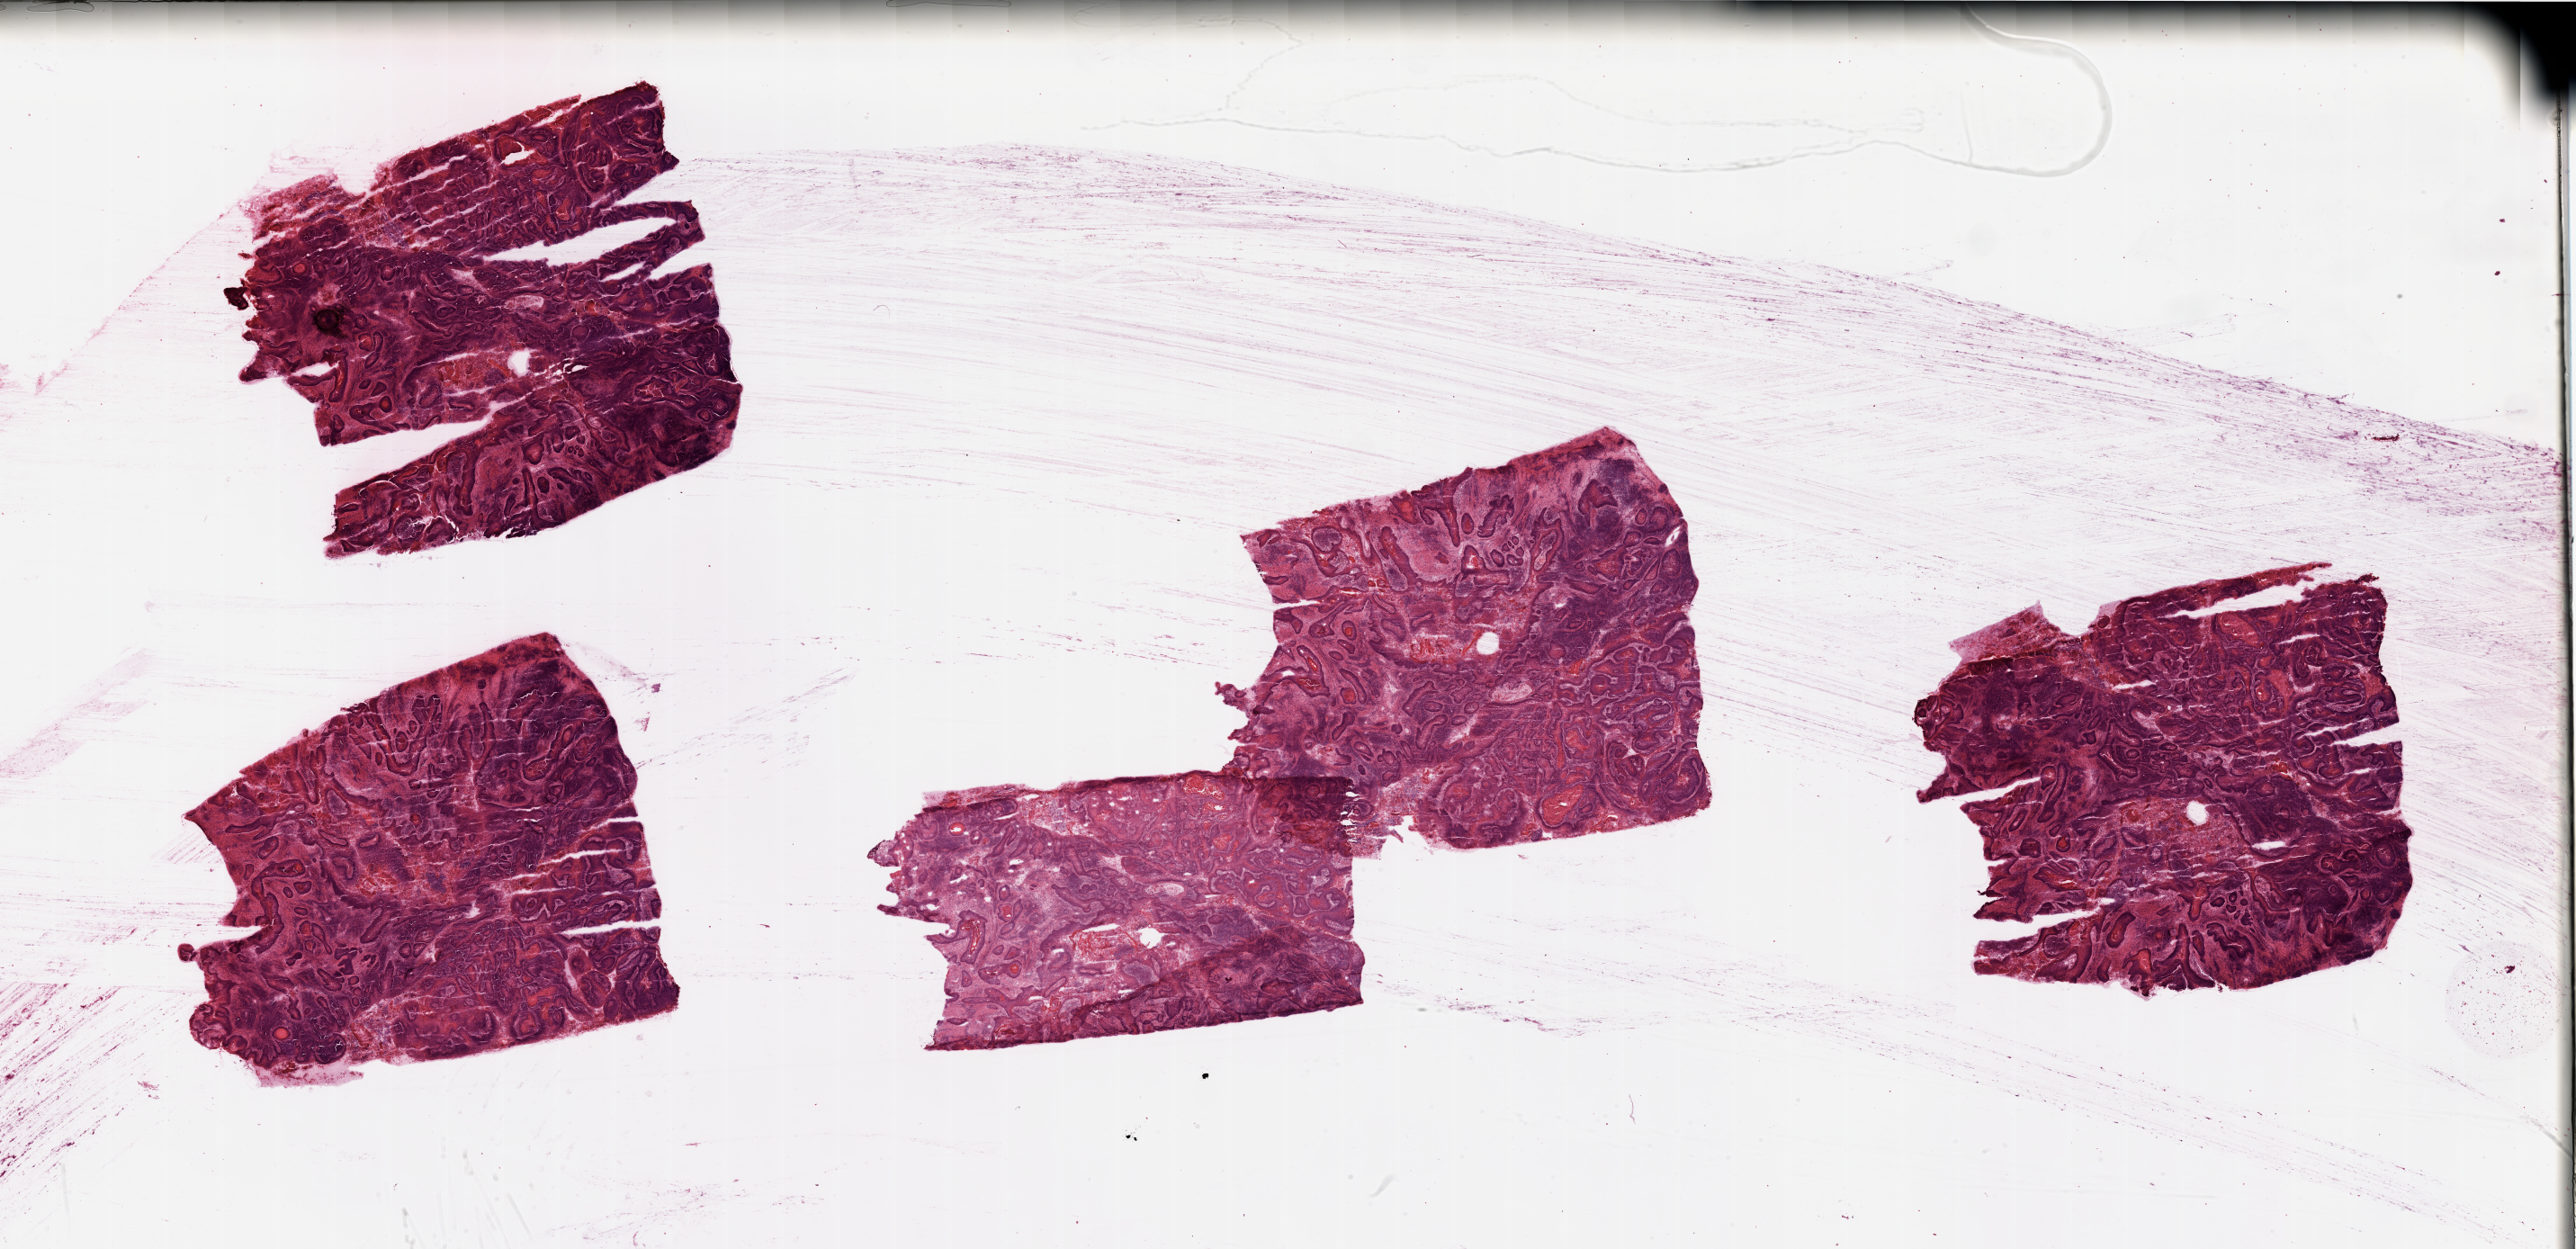
H&E whole-slide image — shown as a low-resolution overview of the whole scanned area (about 45.3 x 22.0 mm). Tumour tissue sample, sampled site: larynx. Patient: male, age 67 years. Histologic grade: G2 (moderately differentiated). Slide review estimates, as recorded: tumour nuclei 85%, necrosis 15%.
Primary tumour site (as recorded): larynx. Diagnosis: Squamous cell carcinoma, NOS (larynx, NOS). AJCC pathologic stage: II.